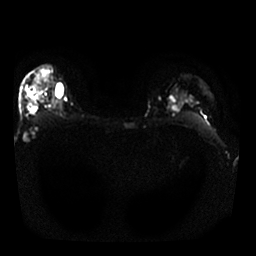
Breast MRI, one axial slice. Position 21 of 30 along the scan axis. Diffusion-weighted series; image 2 of 4 stored at this slice position (different b-values; order by instance number). 1.5 T. 4 mm slice thickness. 256 × 256 image matrix, field of view 340 × 340 mm. Female patient.
Structures marked on this image (manually delineated by an expert):
- tumour on diffusion-weighted imaging: bounding box [x1, y1, x2, y2] px = [40, 74, 51, 81]